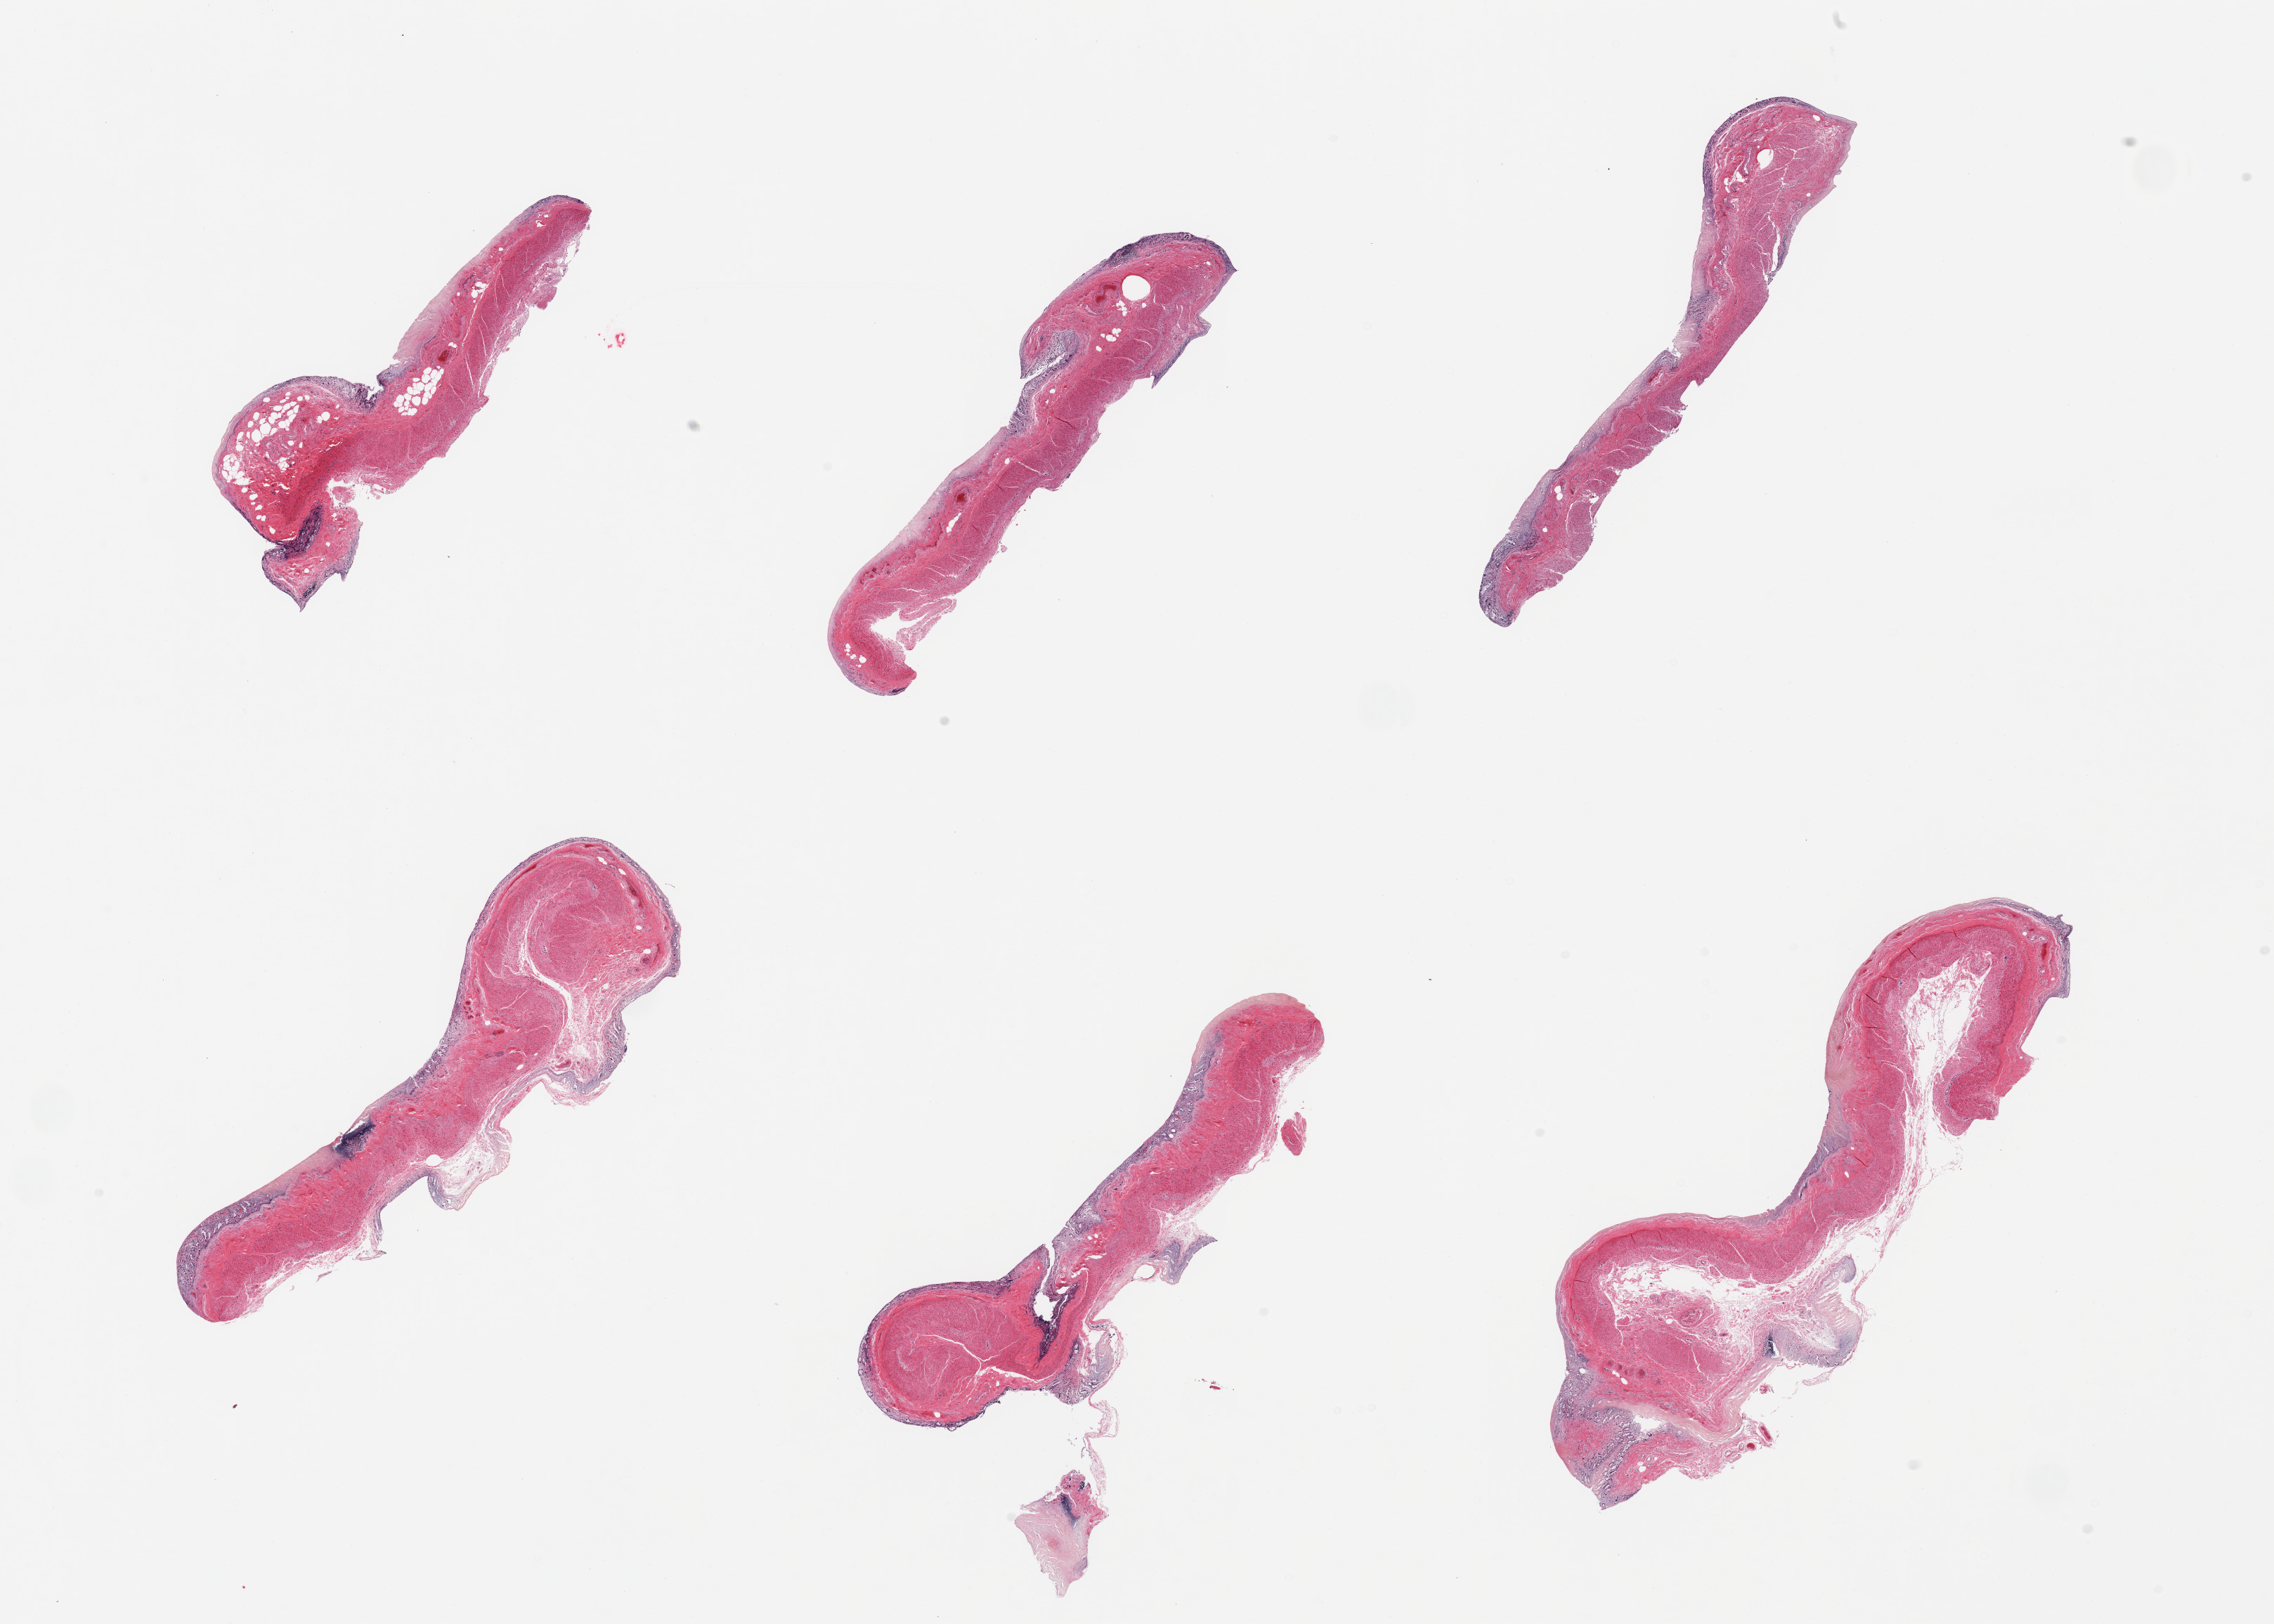
Digitized H&E-stained section, brightfield — shown as a low-resolution overview of the whole scanned area (about 25.6 x 18.3 mm, acquisition: 20x scan). PAXgene-fixed, paraffin-embedded tissue. Section of transverse colon (target tissue). Tissue donor sample. Female donor.
Review note (as recorded): 6 pieces; totally autolyzed mucosa; intact muscularis.